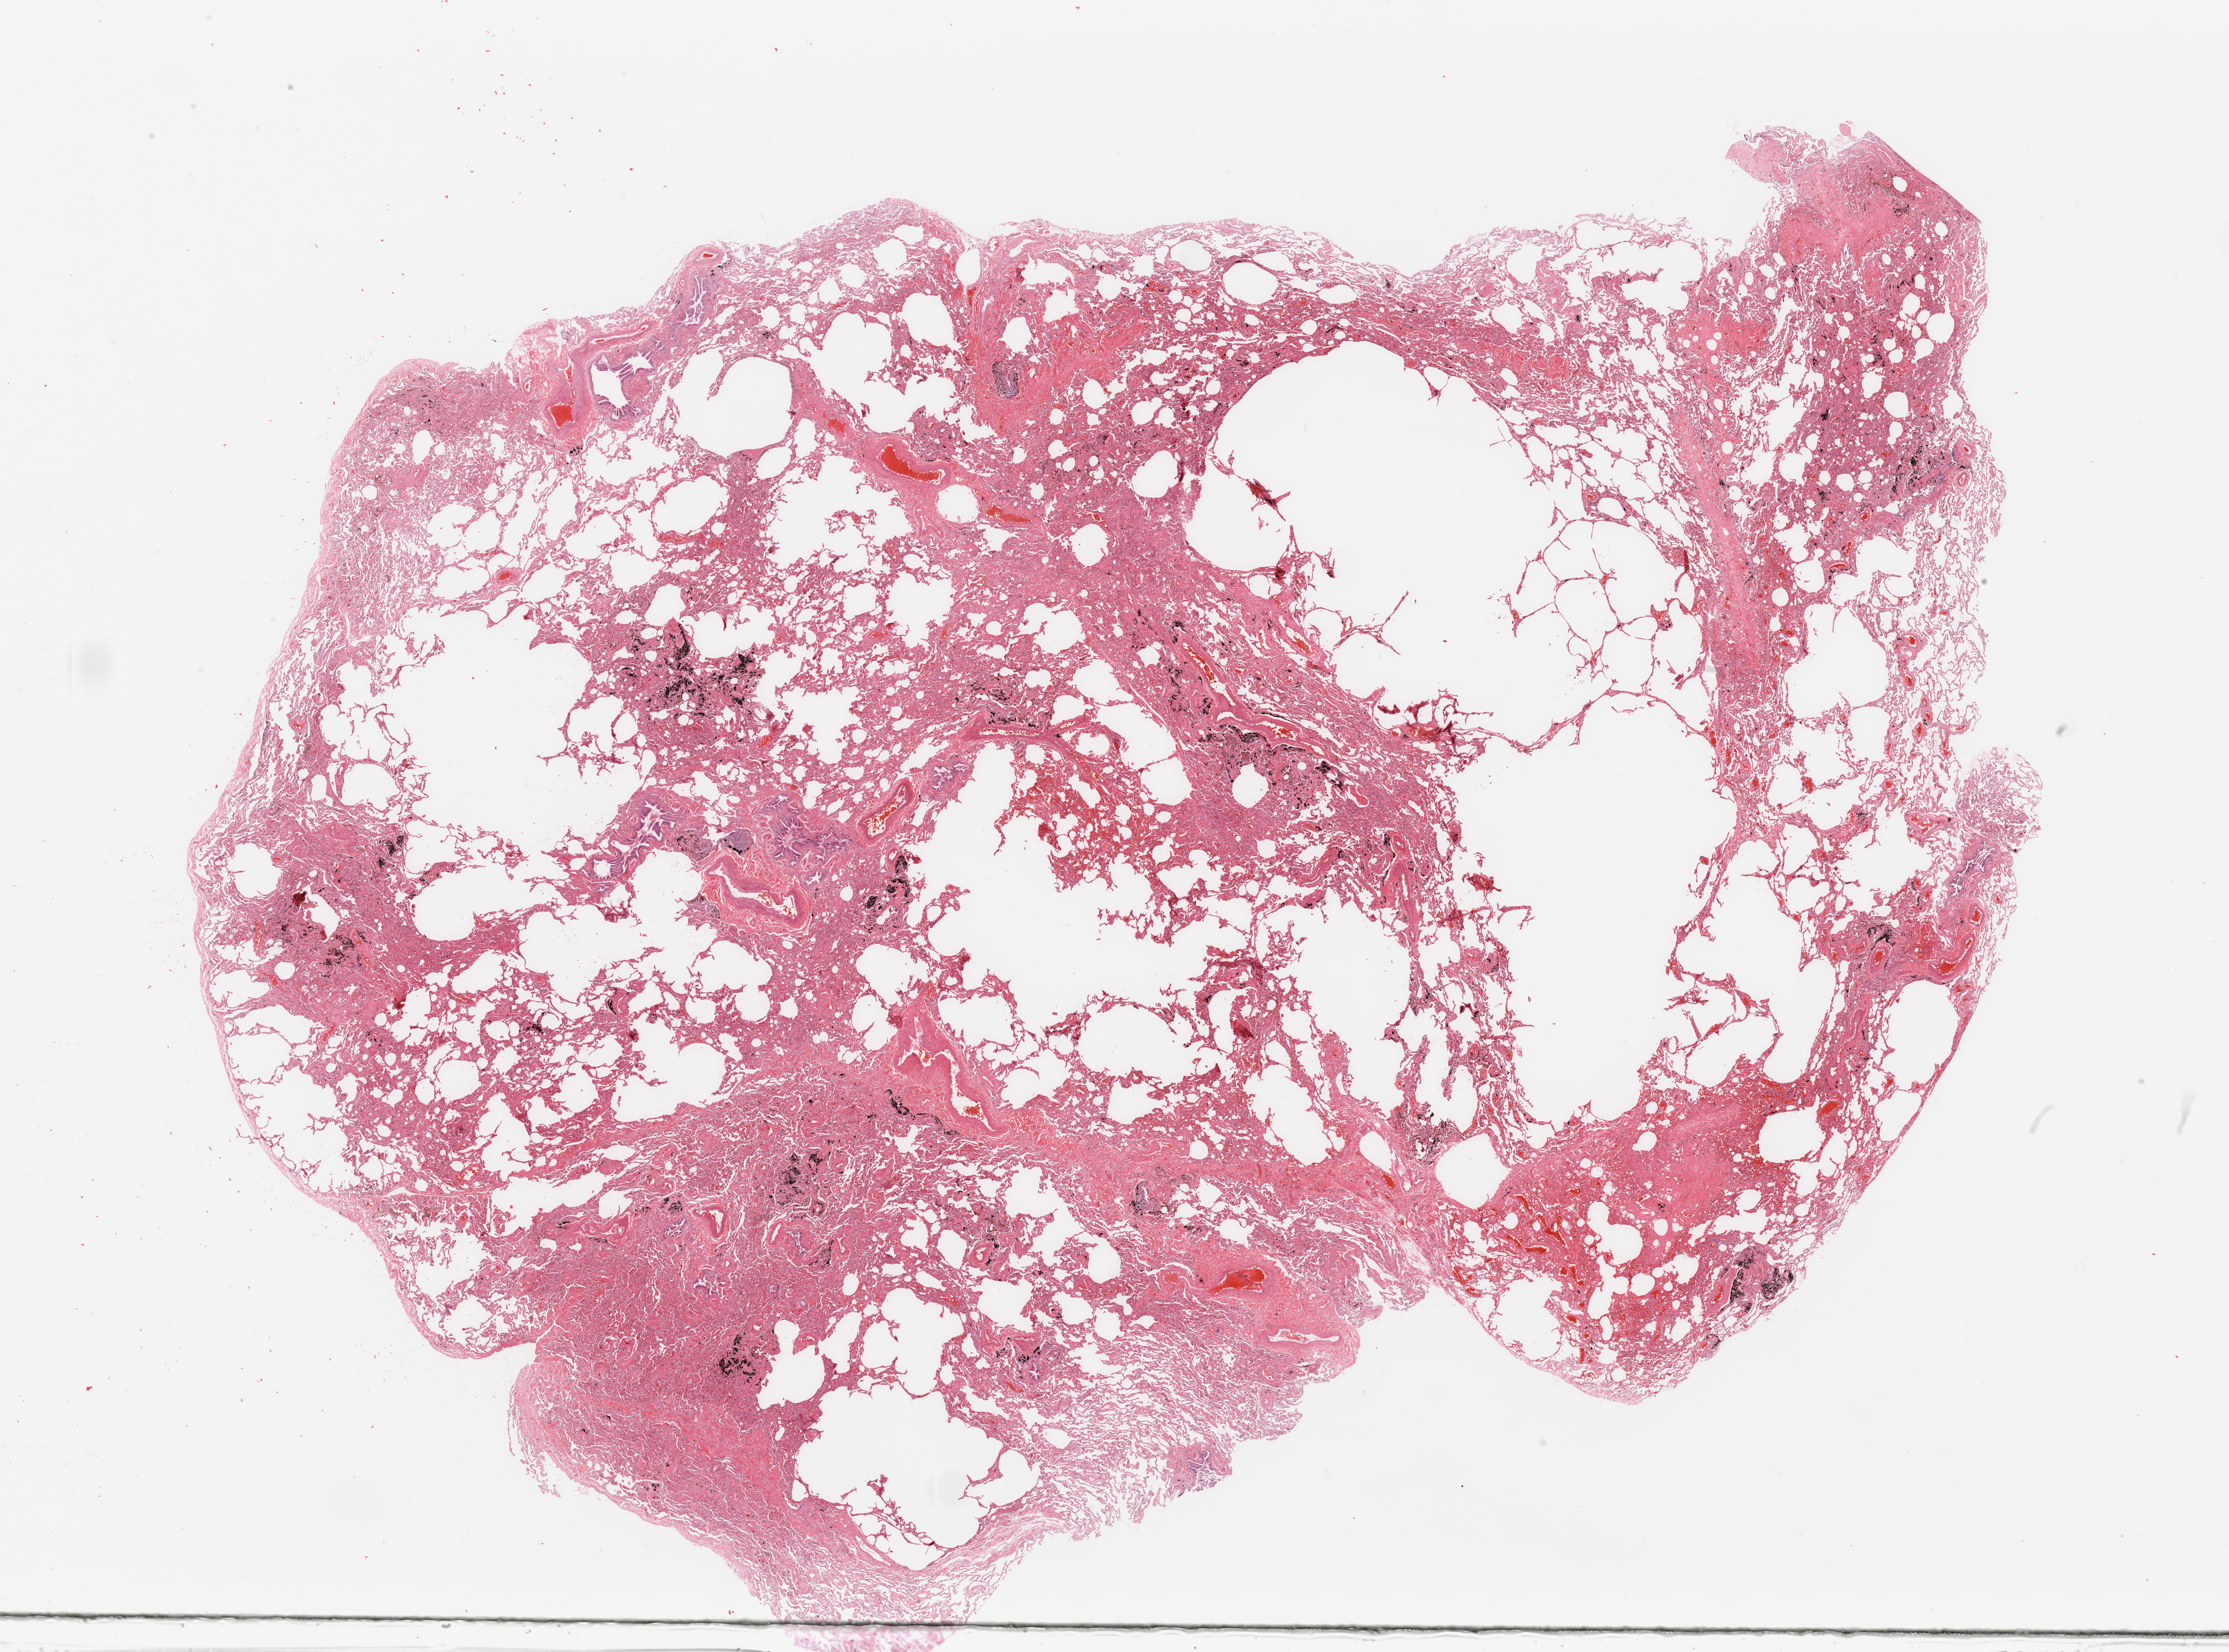
H&E-stained whole-slide image — low-resolution overview of the scanned area, about 30.5 x 22.6 mm; normal (non-tumour) tissue sample, lung. 56-year-old male patient.
This section: normal (non-tumour) tissue from the same patient. Patient diagnosis: Adenocarcinoma, NOS.